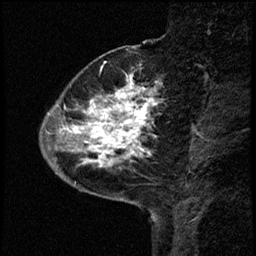
Breast MRI (dynamic contrast-enhanced), one sagittal slice; slice 16 of 68 in the series (ordered by position); dynamic contrast-enhanced study with each time point stored as its own series, time point 2 of 3 at this slice position (early post-contrast, ordered by acquisition time); 1.5 T; TE 4.2 ms, TR 17.6 ms; 2 mm slice thickness; 256 × 256 image matrix, field of view 200 × 200 mm. Female patient, age 52 years. From the clinical record (not read from this slice): setting: breast cancer imaged before/during neoadjuvant chemotherapy; receptor status: HER2-positive.
Outlined on this slice (semi-automatically segmented with operator editing):
- analysis volume of interest (the breast-tissue region the enhancement analysis was run in; not a lesion): bounding box [x1, y1, x2, y2] px = [50, 61, 163, 184]
- tumour enhancement mask (voxels above the 100 % enhancement threshold inside the analysis volume of interest): [53, 74, 159, 167]